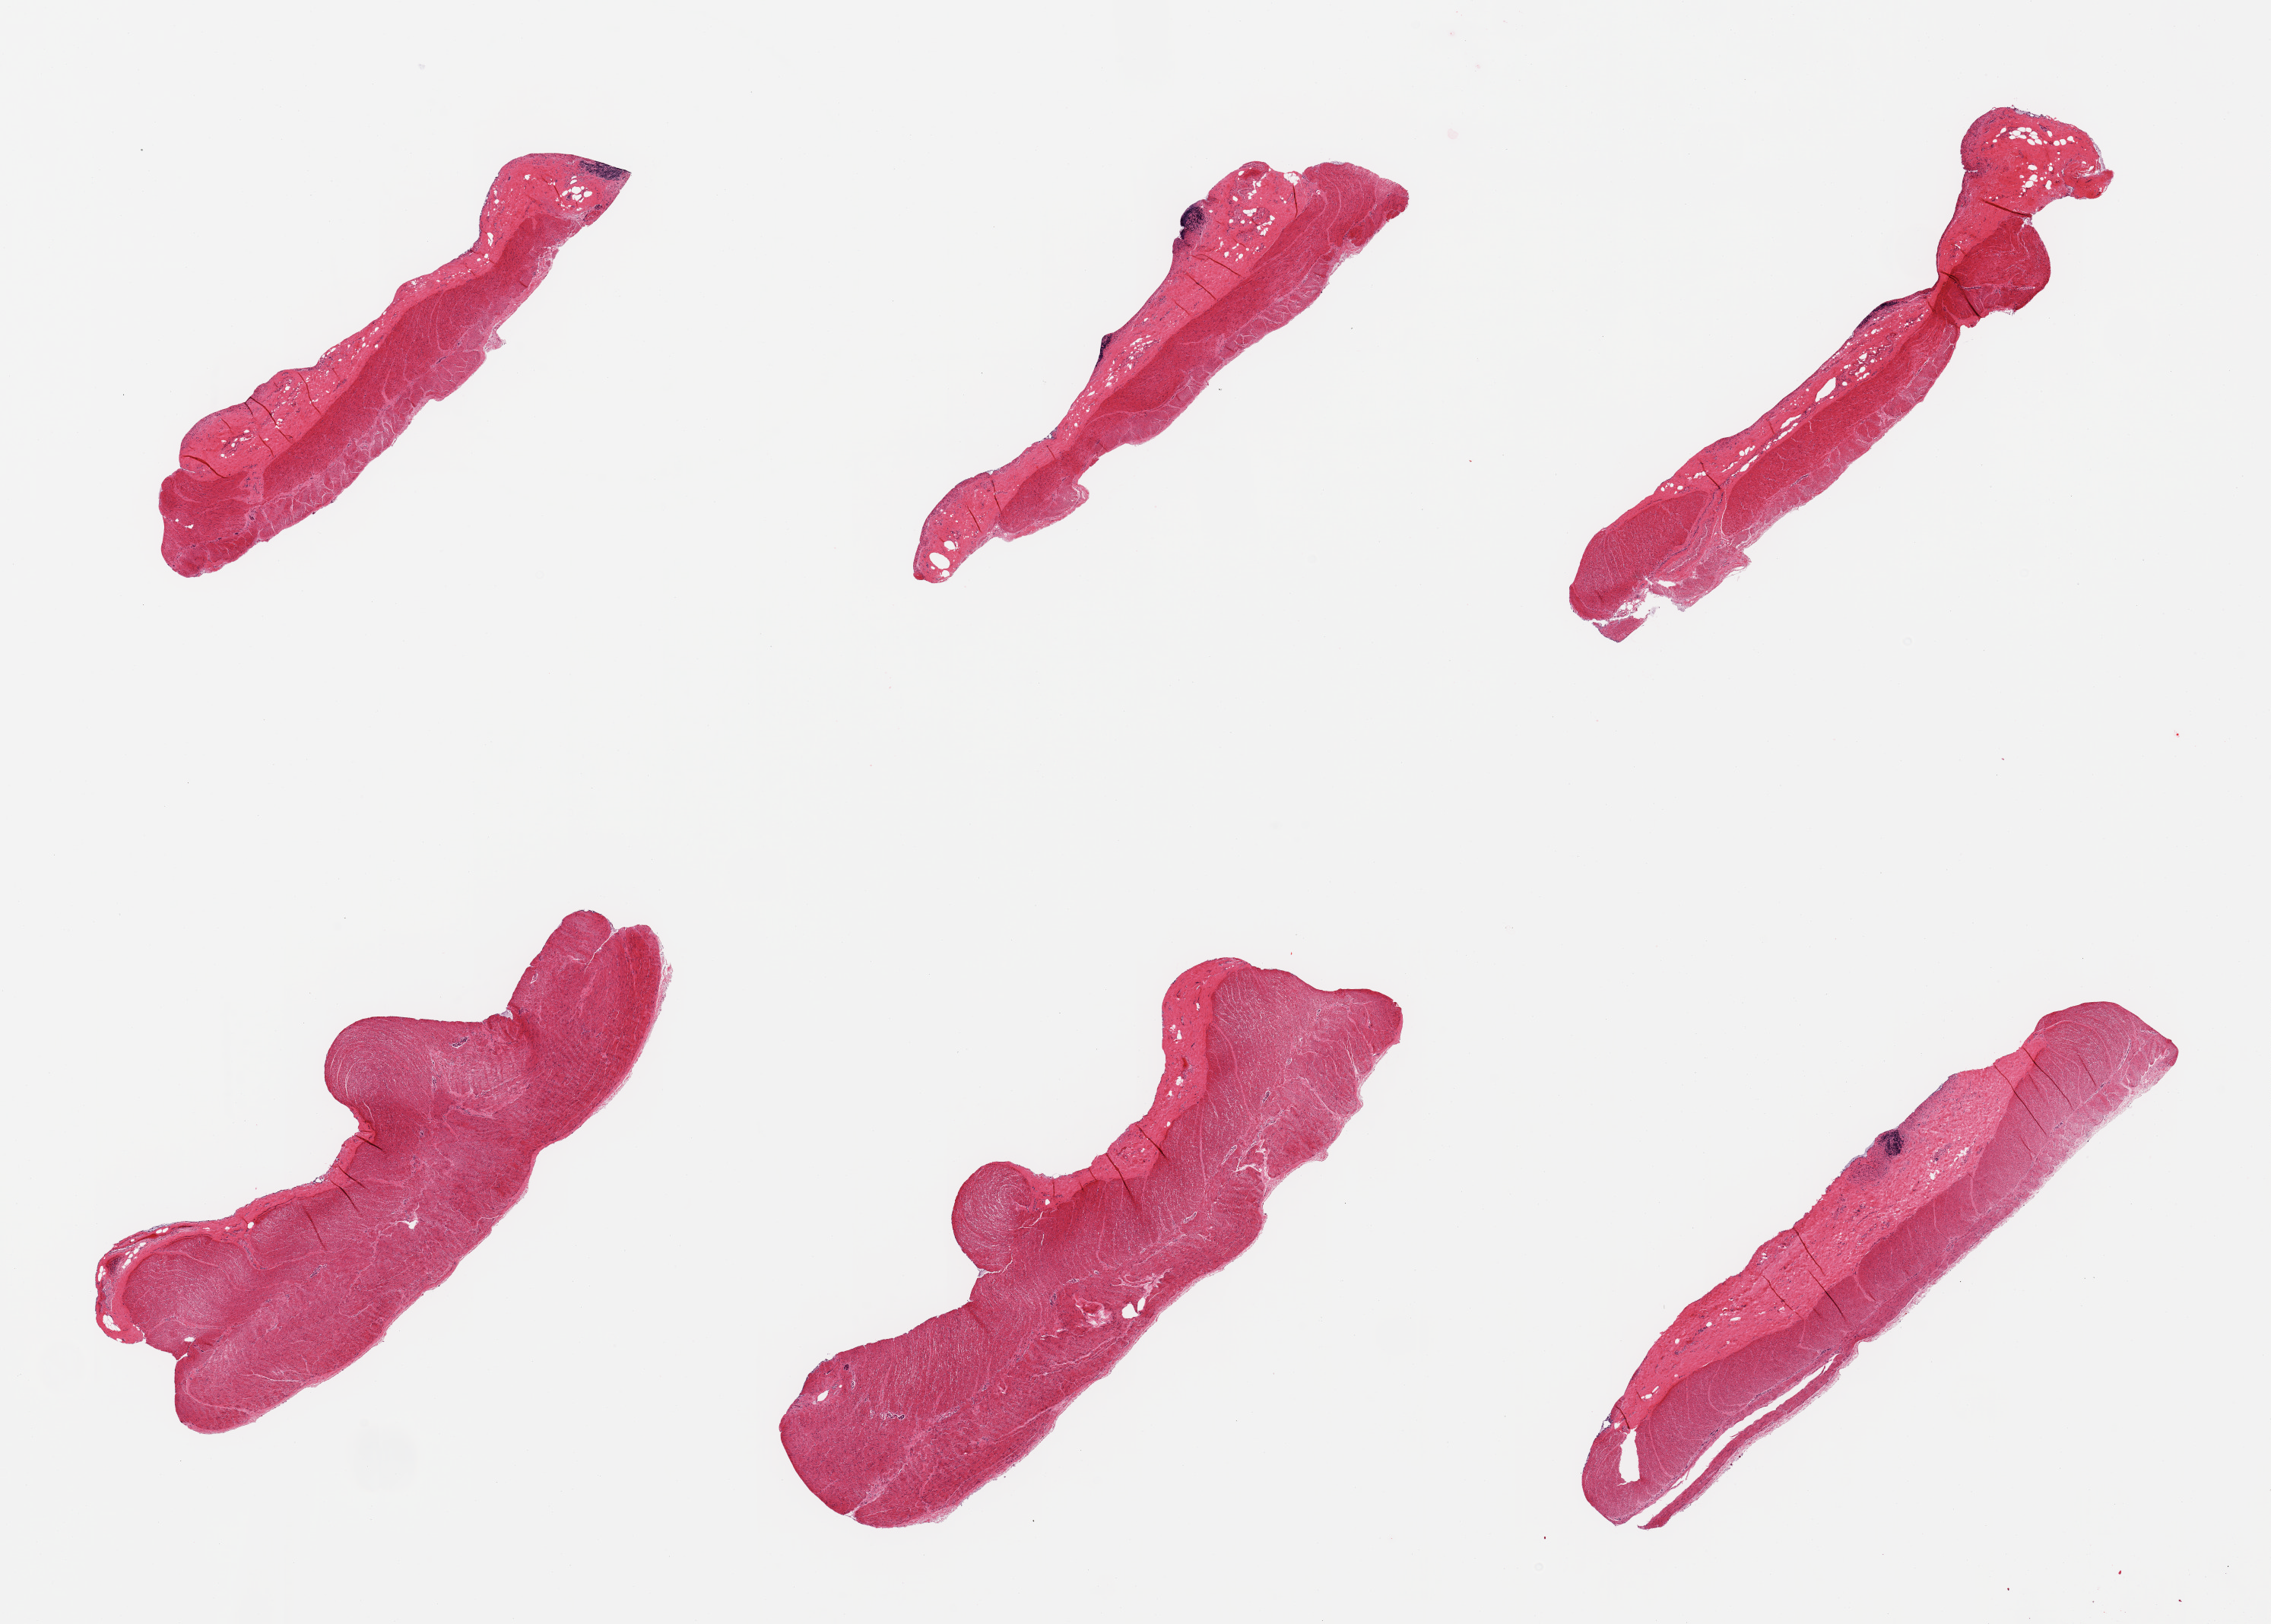
Whole-slide image, H&E stain, whole scanned area (about 23.6 x 16.9 mm) shown as a low-resolution overview; PAXgene-fixed paraffin-embedded (PFPE) section; target tissue: sigmoid colon; tissue donor sample. Donor: male.
* reviewer comment on this tissue sample: 6 pieces; target muscularis propria and ~0.9mm submucosa with scattered lymphoid aggregates